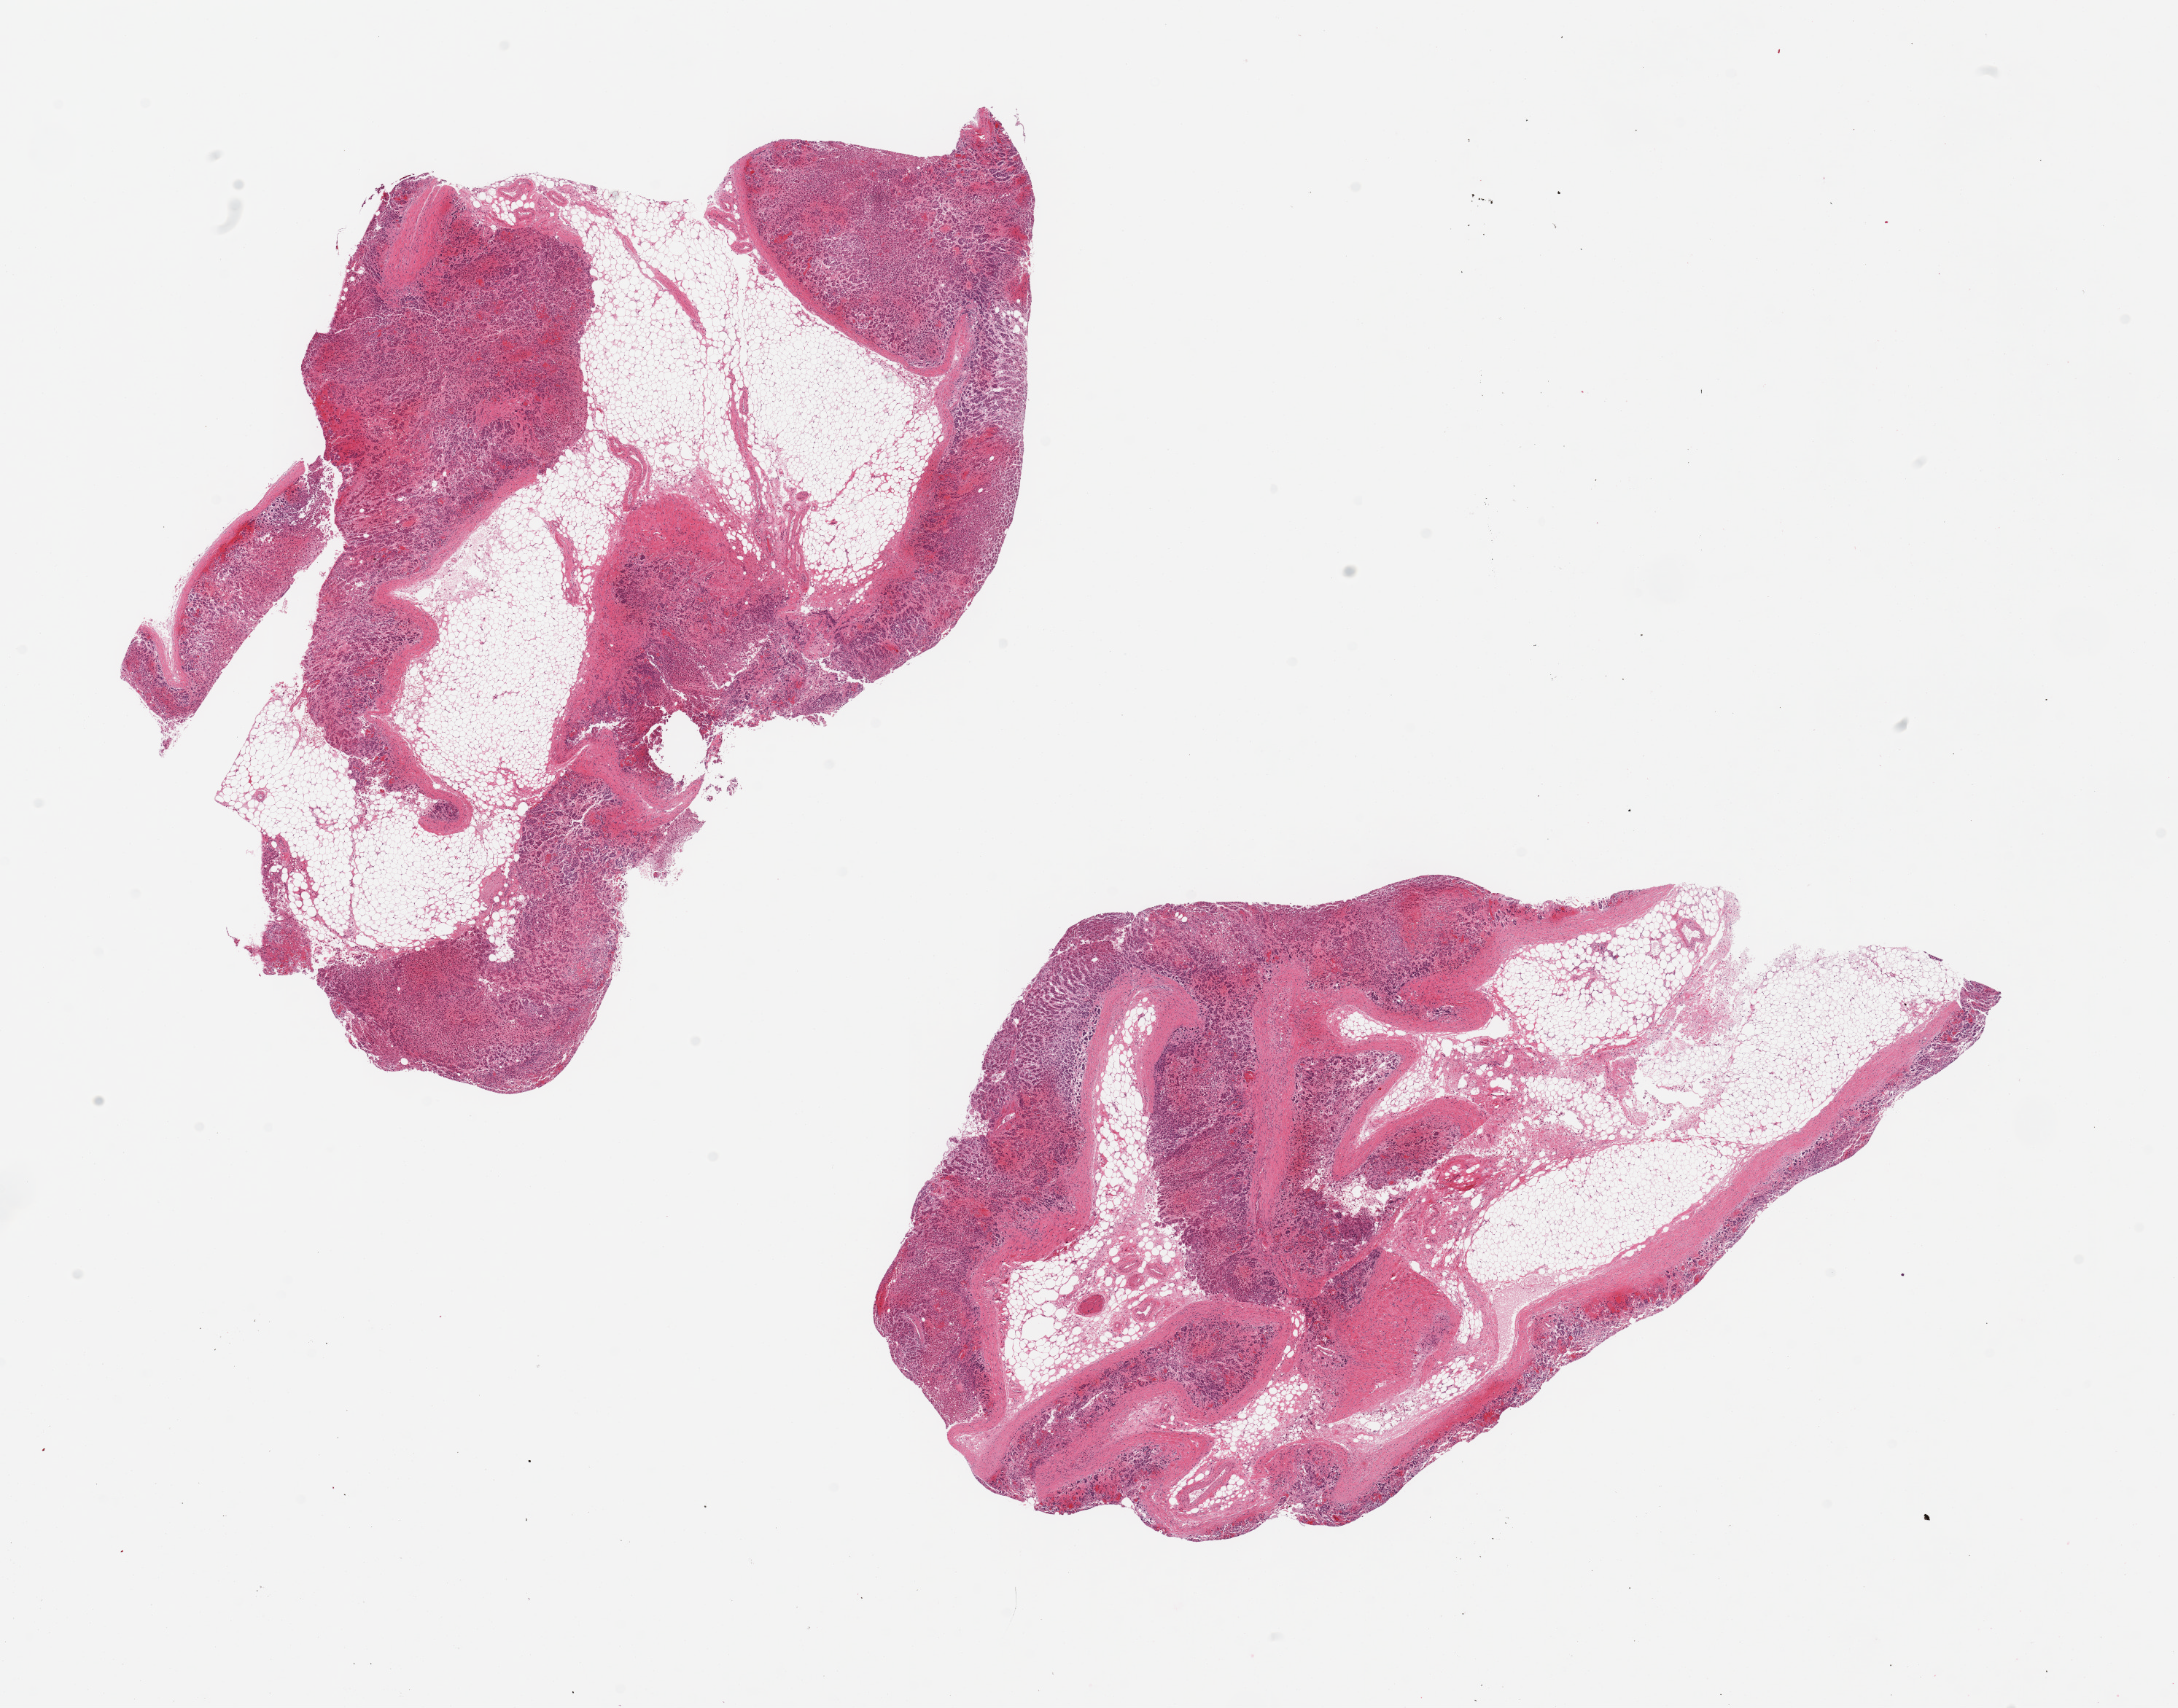
Haematoxylin and eosin whole-slide image — whole scanned area (about 23.6 x 18.5 mm) shown as a low-resolution overview, PAXgene-fixed, paraffin-embedded tissue, section of adrenal gland (target tissue), donor tissue sample. Female donor.
- review note (as recorded): 2 pieces; 50% internal fat